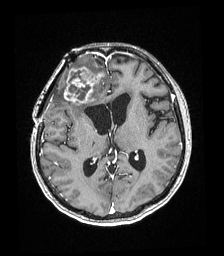
Brain MRI from a brain-tumour surgery series, one axial slice. Slice 94 of 192 in the series (ordered by position). T1-weighted post-contrast. 224 × 256 image matrix, field of view 219 × 250 mm. Case-level facts recorded for this patient, not image findings: histopathology: Astrocytoma; WHO grade: 4; IDH mutation: yes; tumour location: Right superficial frontal.
Annotated regions visible in this slice (manually delineated by an expert):
- tumour: bounding box <64,59,101,103> (left, top, right, bottom; pixels)